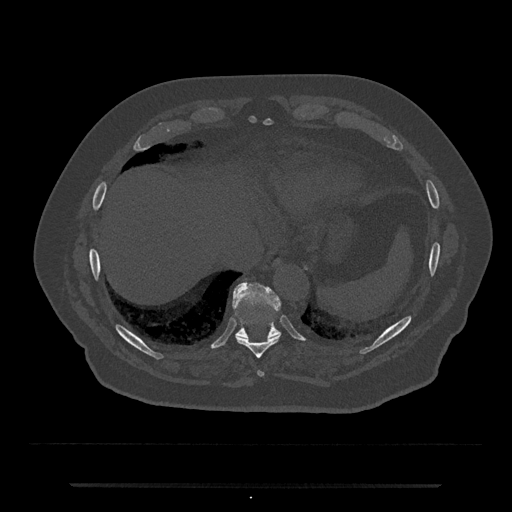
CT including the spine, one axial slice; slice 739 of 797 in the series (ordered by position); reconstruction kernel Br40s/3; 120 kVp; bone window (W 1800 / L 400 HU); 512 × 512 image matrix. Male patient, age 80 years. From the clinical record (not read from this slice): primary cancer: prostate; vertebrae with lytic lesions (as recorded): L1, T11.
Structures marked on this image (semi-automatic segmentation, software-assisted and operator-edited):
- T10 vertebra: bounding box [x1, y1, x2, y2] px = [233, 283, 281, 338]
- T8 vertebra: [258, 371, 264, 376]
- T9 vertebra: [236, 335, 280, 359]